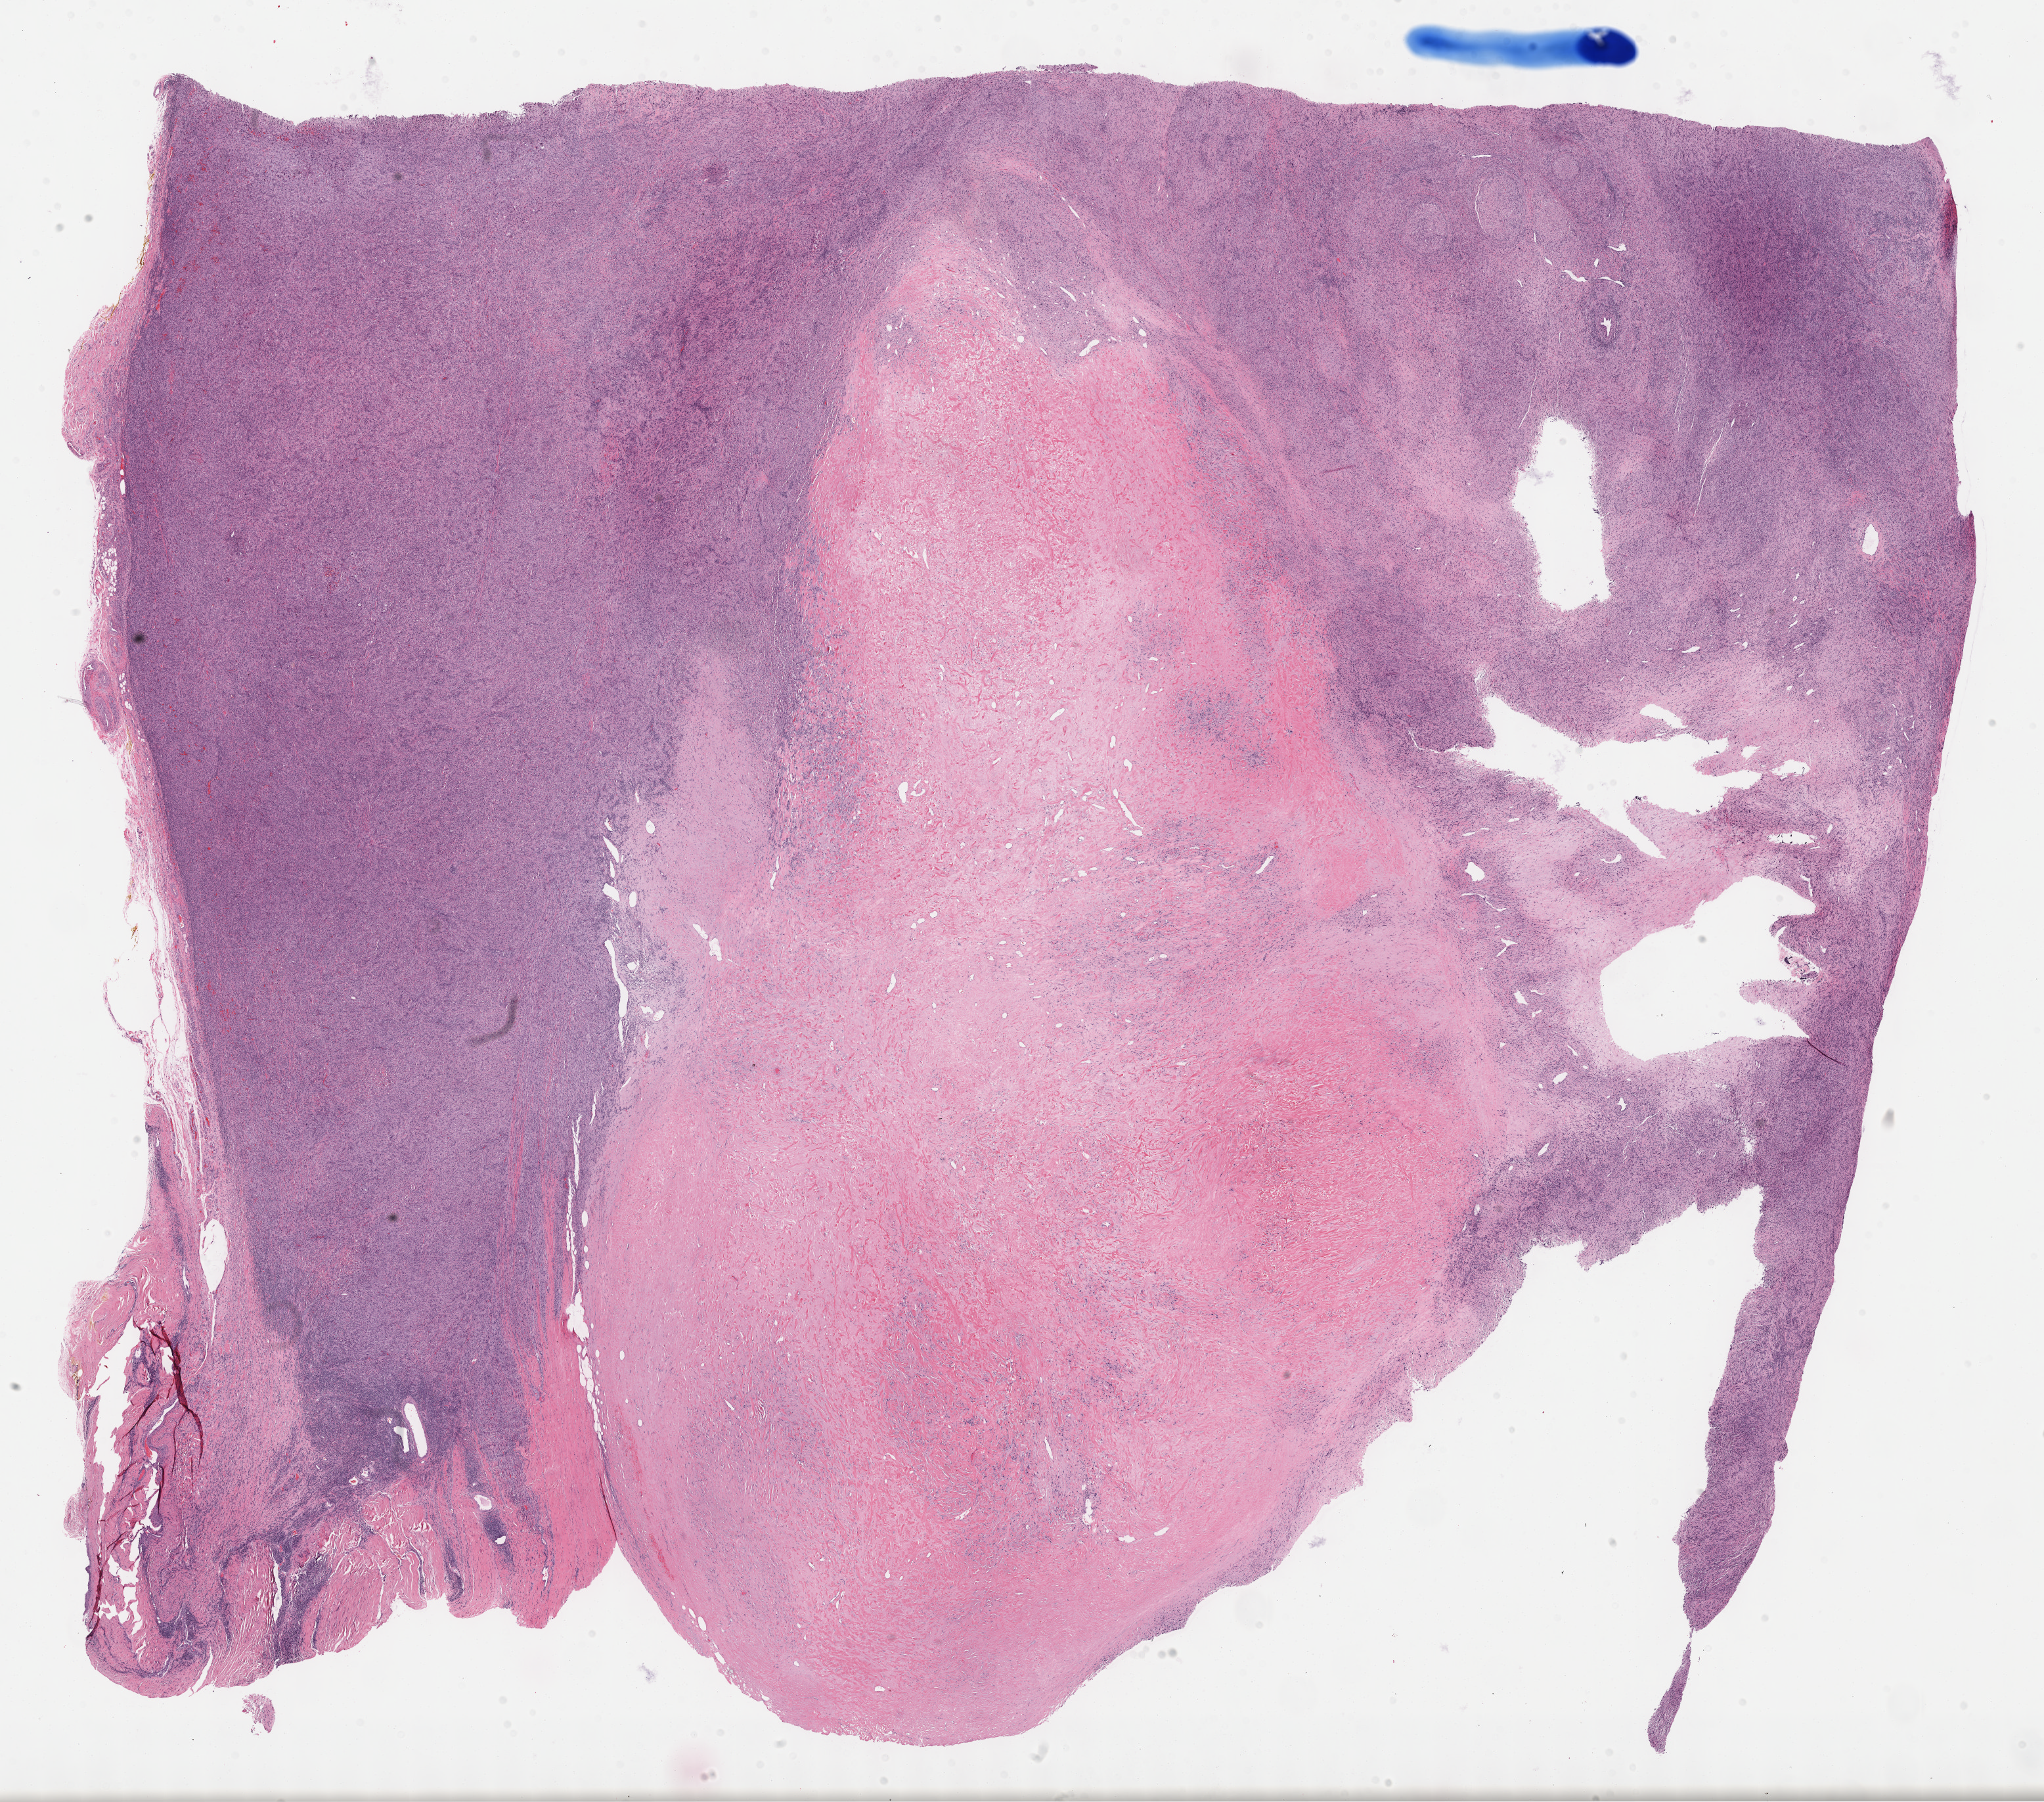
H&E-stained whole-slide image, whole scanned area (about 25.2 x 22.2 mm, acquisition: 40x scan) shown as a low-resolution overview, formalin-fixed paraffin-embedded (FFPE) diagnostic section, primary tumour sample from the connective, subcutaneous and other soft tissues. Patient sex: female.
- diagnosis: Malignant fibrous histiocytoma